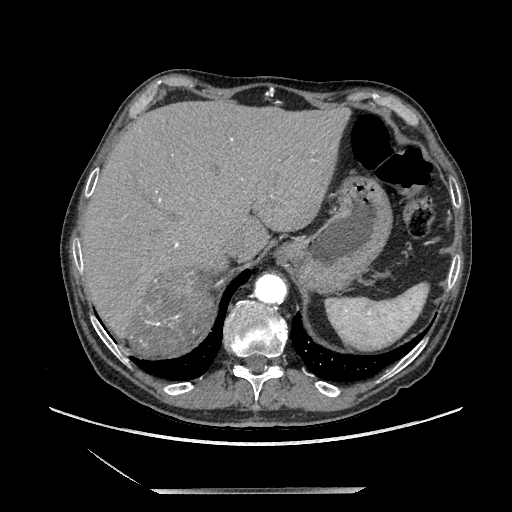
Contrast-enhanced abdominal CT, one axial slice; position 170 of 243 along the scan axis; soft-tissue window (W 400 / L 40 HU); 1.25 mm slice thickness; 512 × 512 image matrix, field of view 420 × 420 mm. Male patient. From the clinical record (not read from this slice): diagnosis: adrenocortical carcinoma; tumour side: right adrenal; tumour size at pathology: 16 cm; Ki-67 index: 17 %; stage (as recorded): 3.
Outlined on this slice (semi-automatically segmented with operator editing):
- mass: bounding box [x1, y1, x2, y2] px = [125, 270, 211, 357]